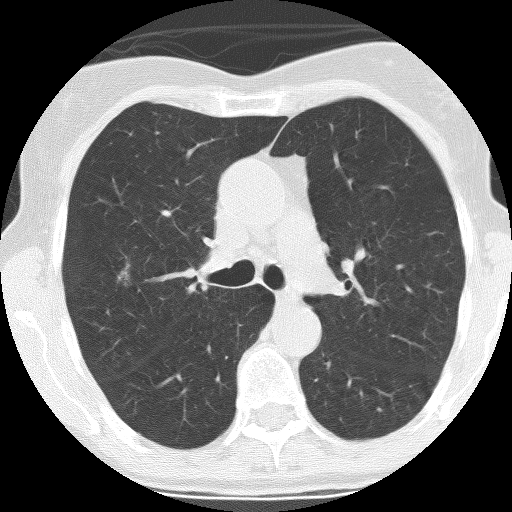
Chest CT (low-dose screening protocol), one axial image. First (baseline) screen. Lung window (W 1500 / L -600 HU). 2.5 mm slice thickness. 120 kVp. 512 × 512 image matrix, field of view 270 × 270 mm. Female, age 68 years at enrolment.
Expert reader's lesion annotation, bounding box [x1, y1, x2, y2] px = [98, 255, 138, 302]. Reader record for this screening exam (exam-level; its link to the box is not recorded): non-calcified nodule or mass ≥4 mm, right upper lobe, 13 × 8 mm, spiculated (stellate) margins, mixed attenuation. Later outcome: lung cancer diagnosed 113 days after this screen — adenocarcinoma, NOS, right upper lobe, moderately differentiated (G2), stage IA (AJCC 6th edition), 10 mm at pathology.